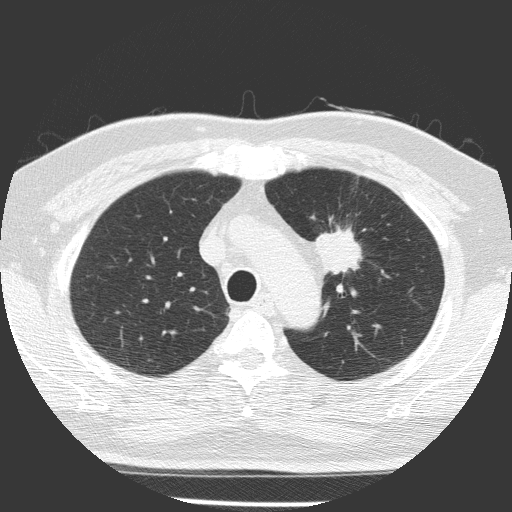
Low-dose screening chest CT, one axial slice; slice 115 of 156 in the series (ordered by position); reconstruction kernel FC51; lung window (W 1500 / L -600 HU); 2 mm slice thickness; 512 × 512 image matrix, field of view 309 × 309 mm.
Structures marked on this image (expert manual segmentation):
- lesion 1 (tumor, upper lobe of left lung): bounding box <315,228,362,274> (left, top, right, bottom; pixels)